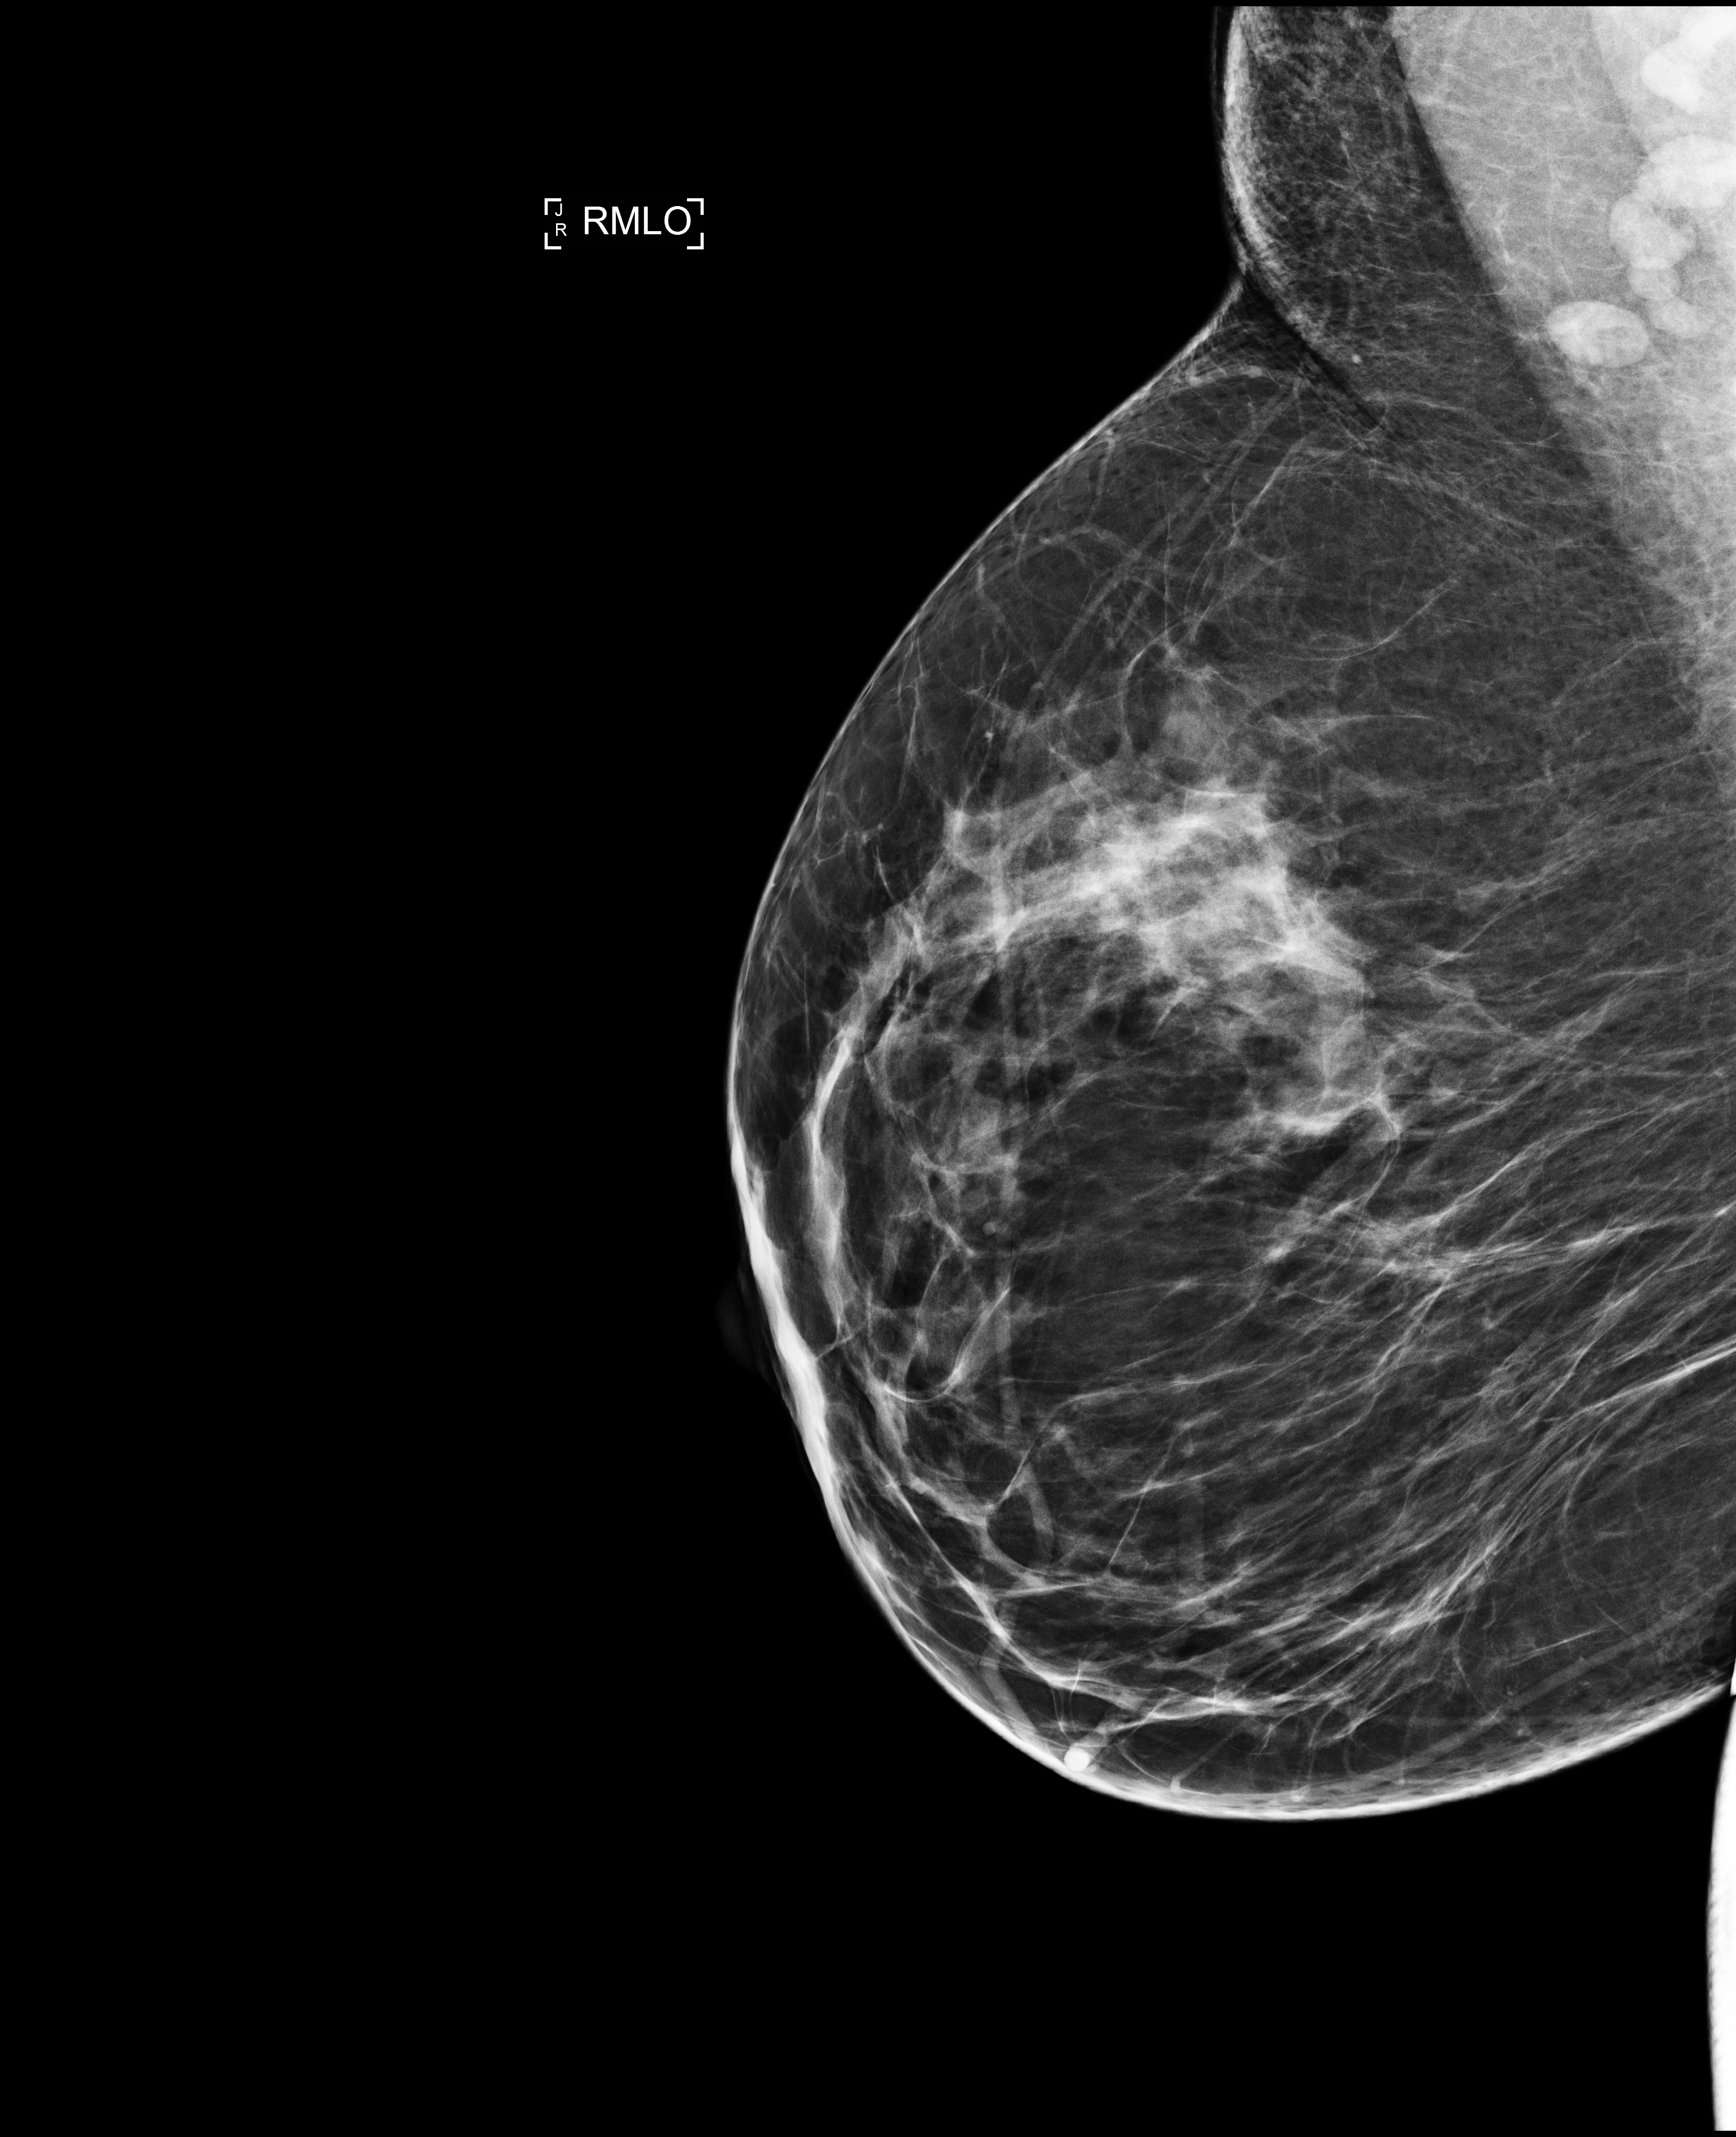
Annual screening mammography examination; system: Selenia Dimensions. Patient: female, 50 years.
Image type: full-field digital mammogram. Breast: right. Projection: medio-lateral oblique projection.